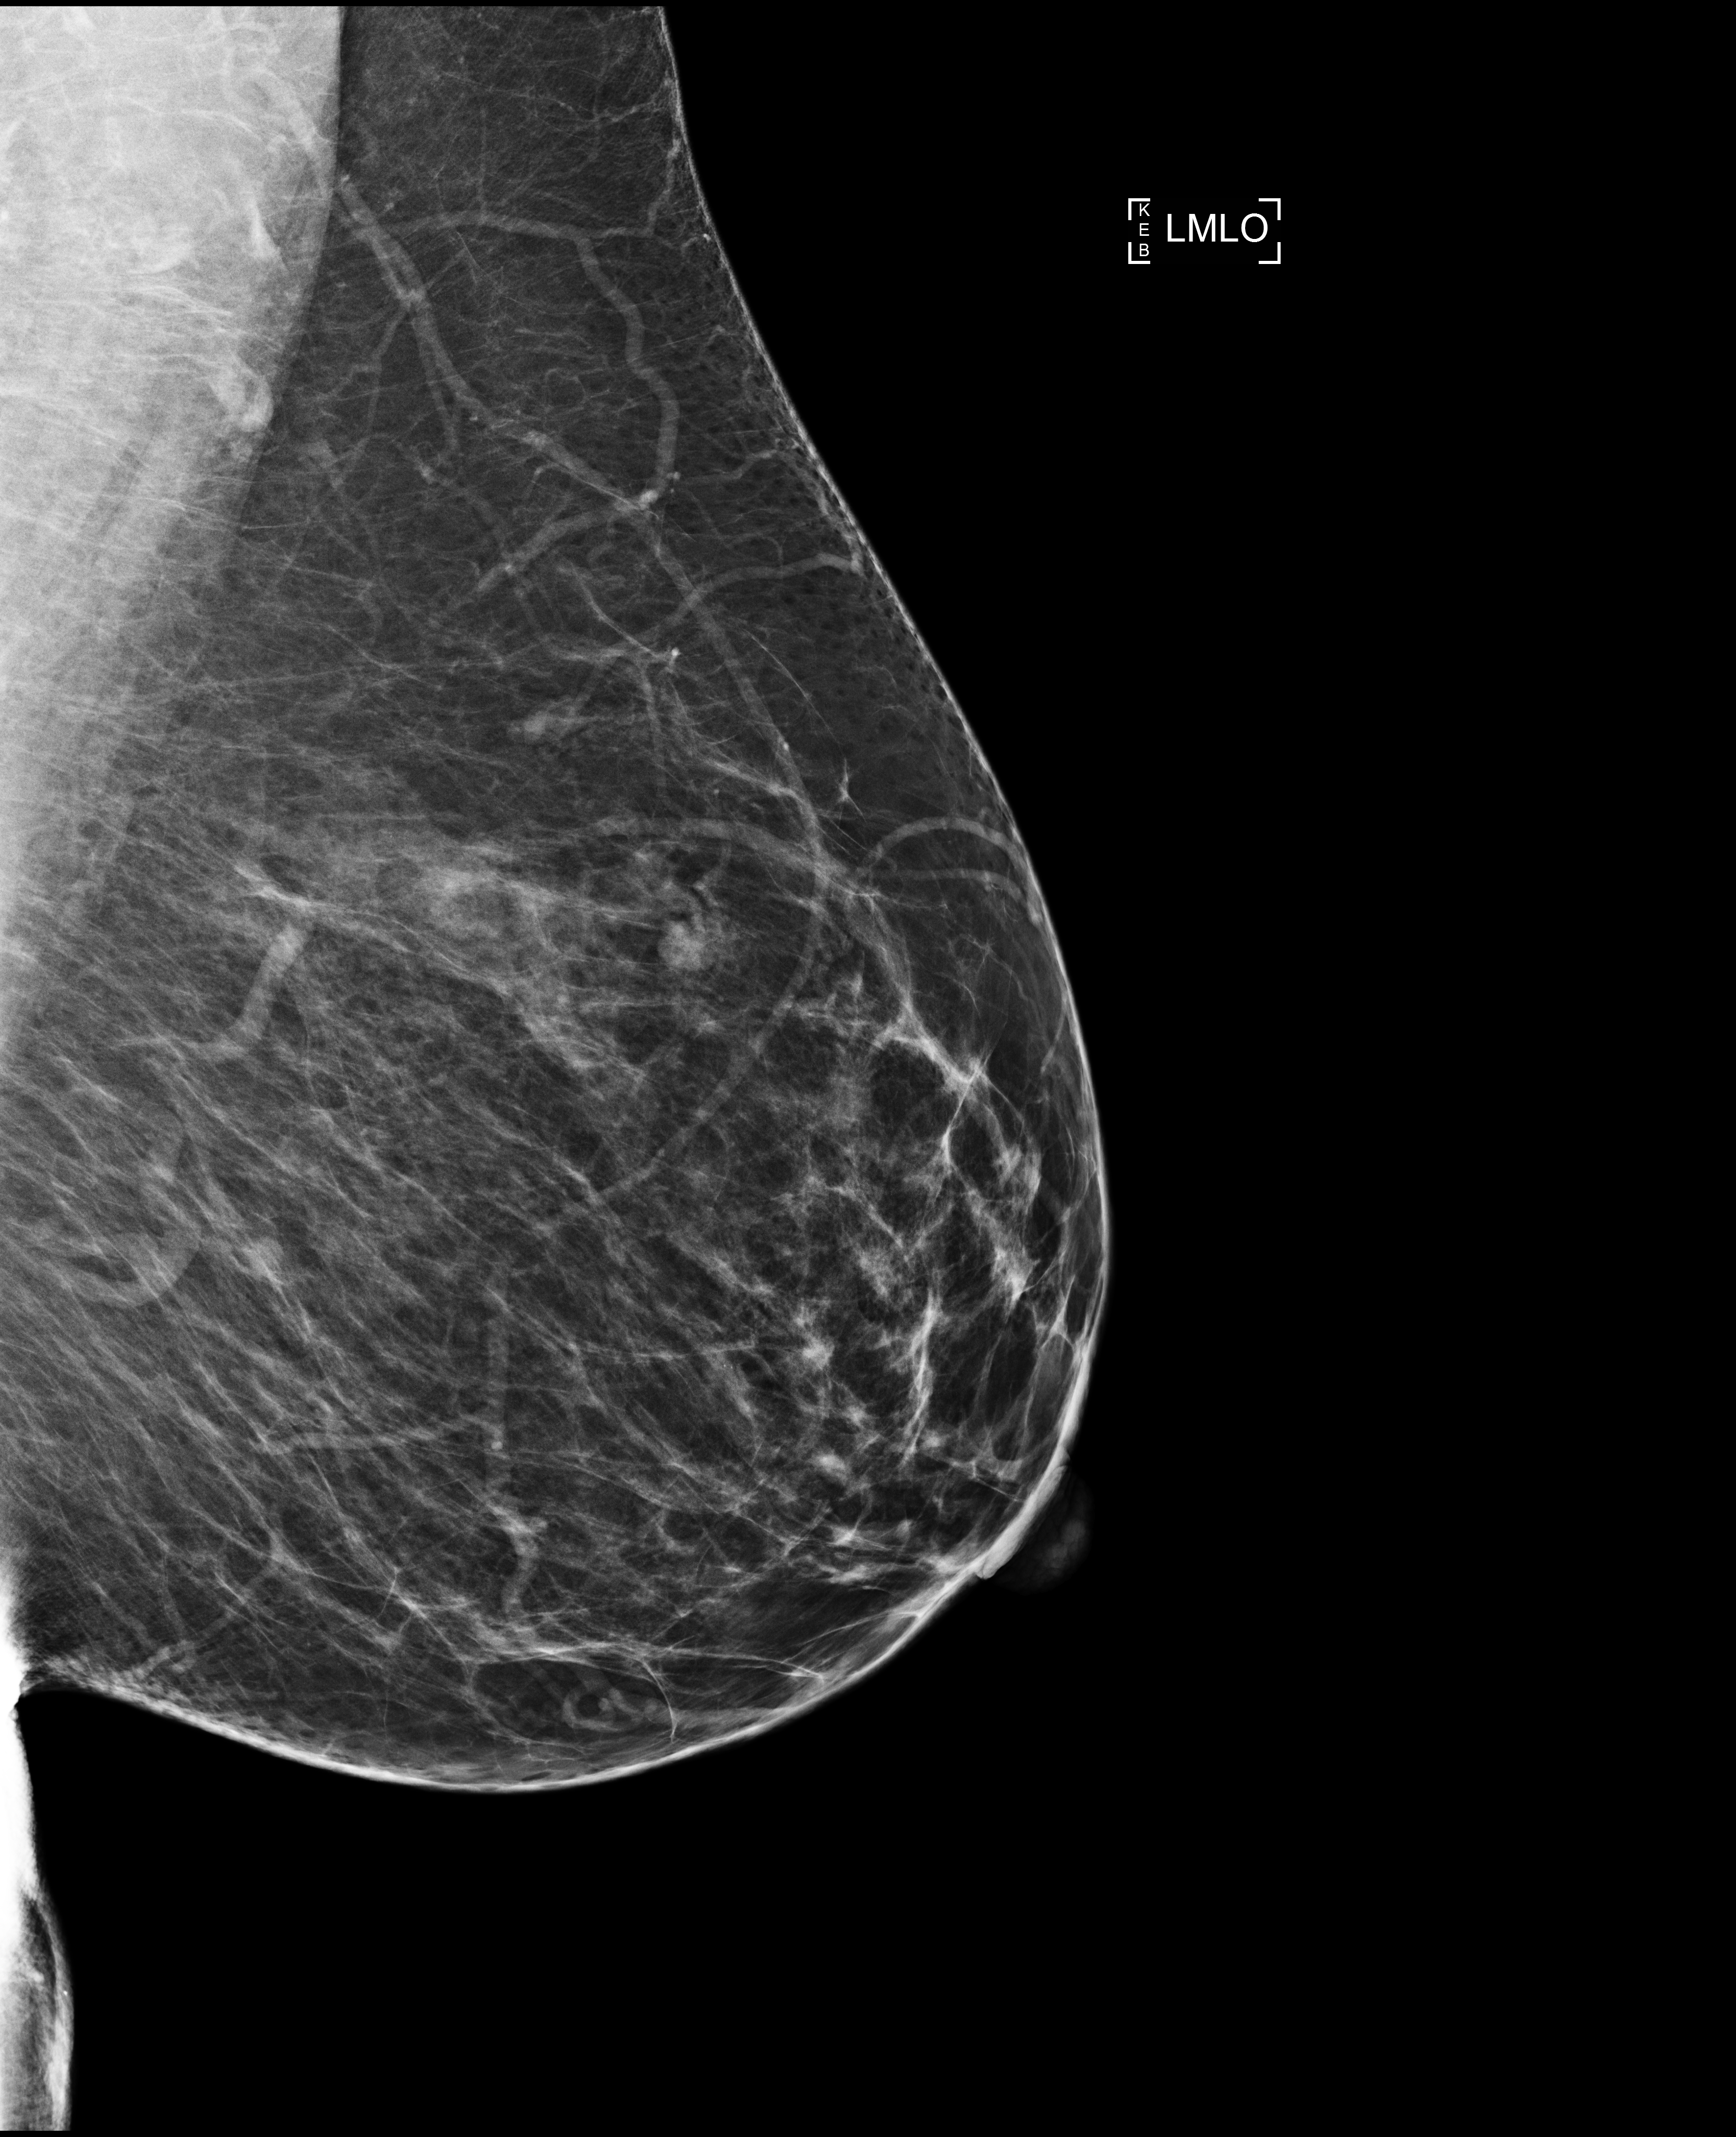
Screening examination. Patient: female, 53 years.
Image type: full-field digital mammogram. Breast: left. Projection: MLO view.